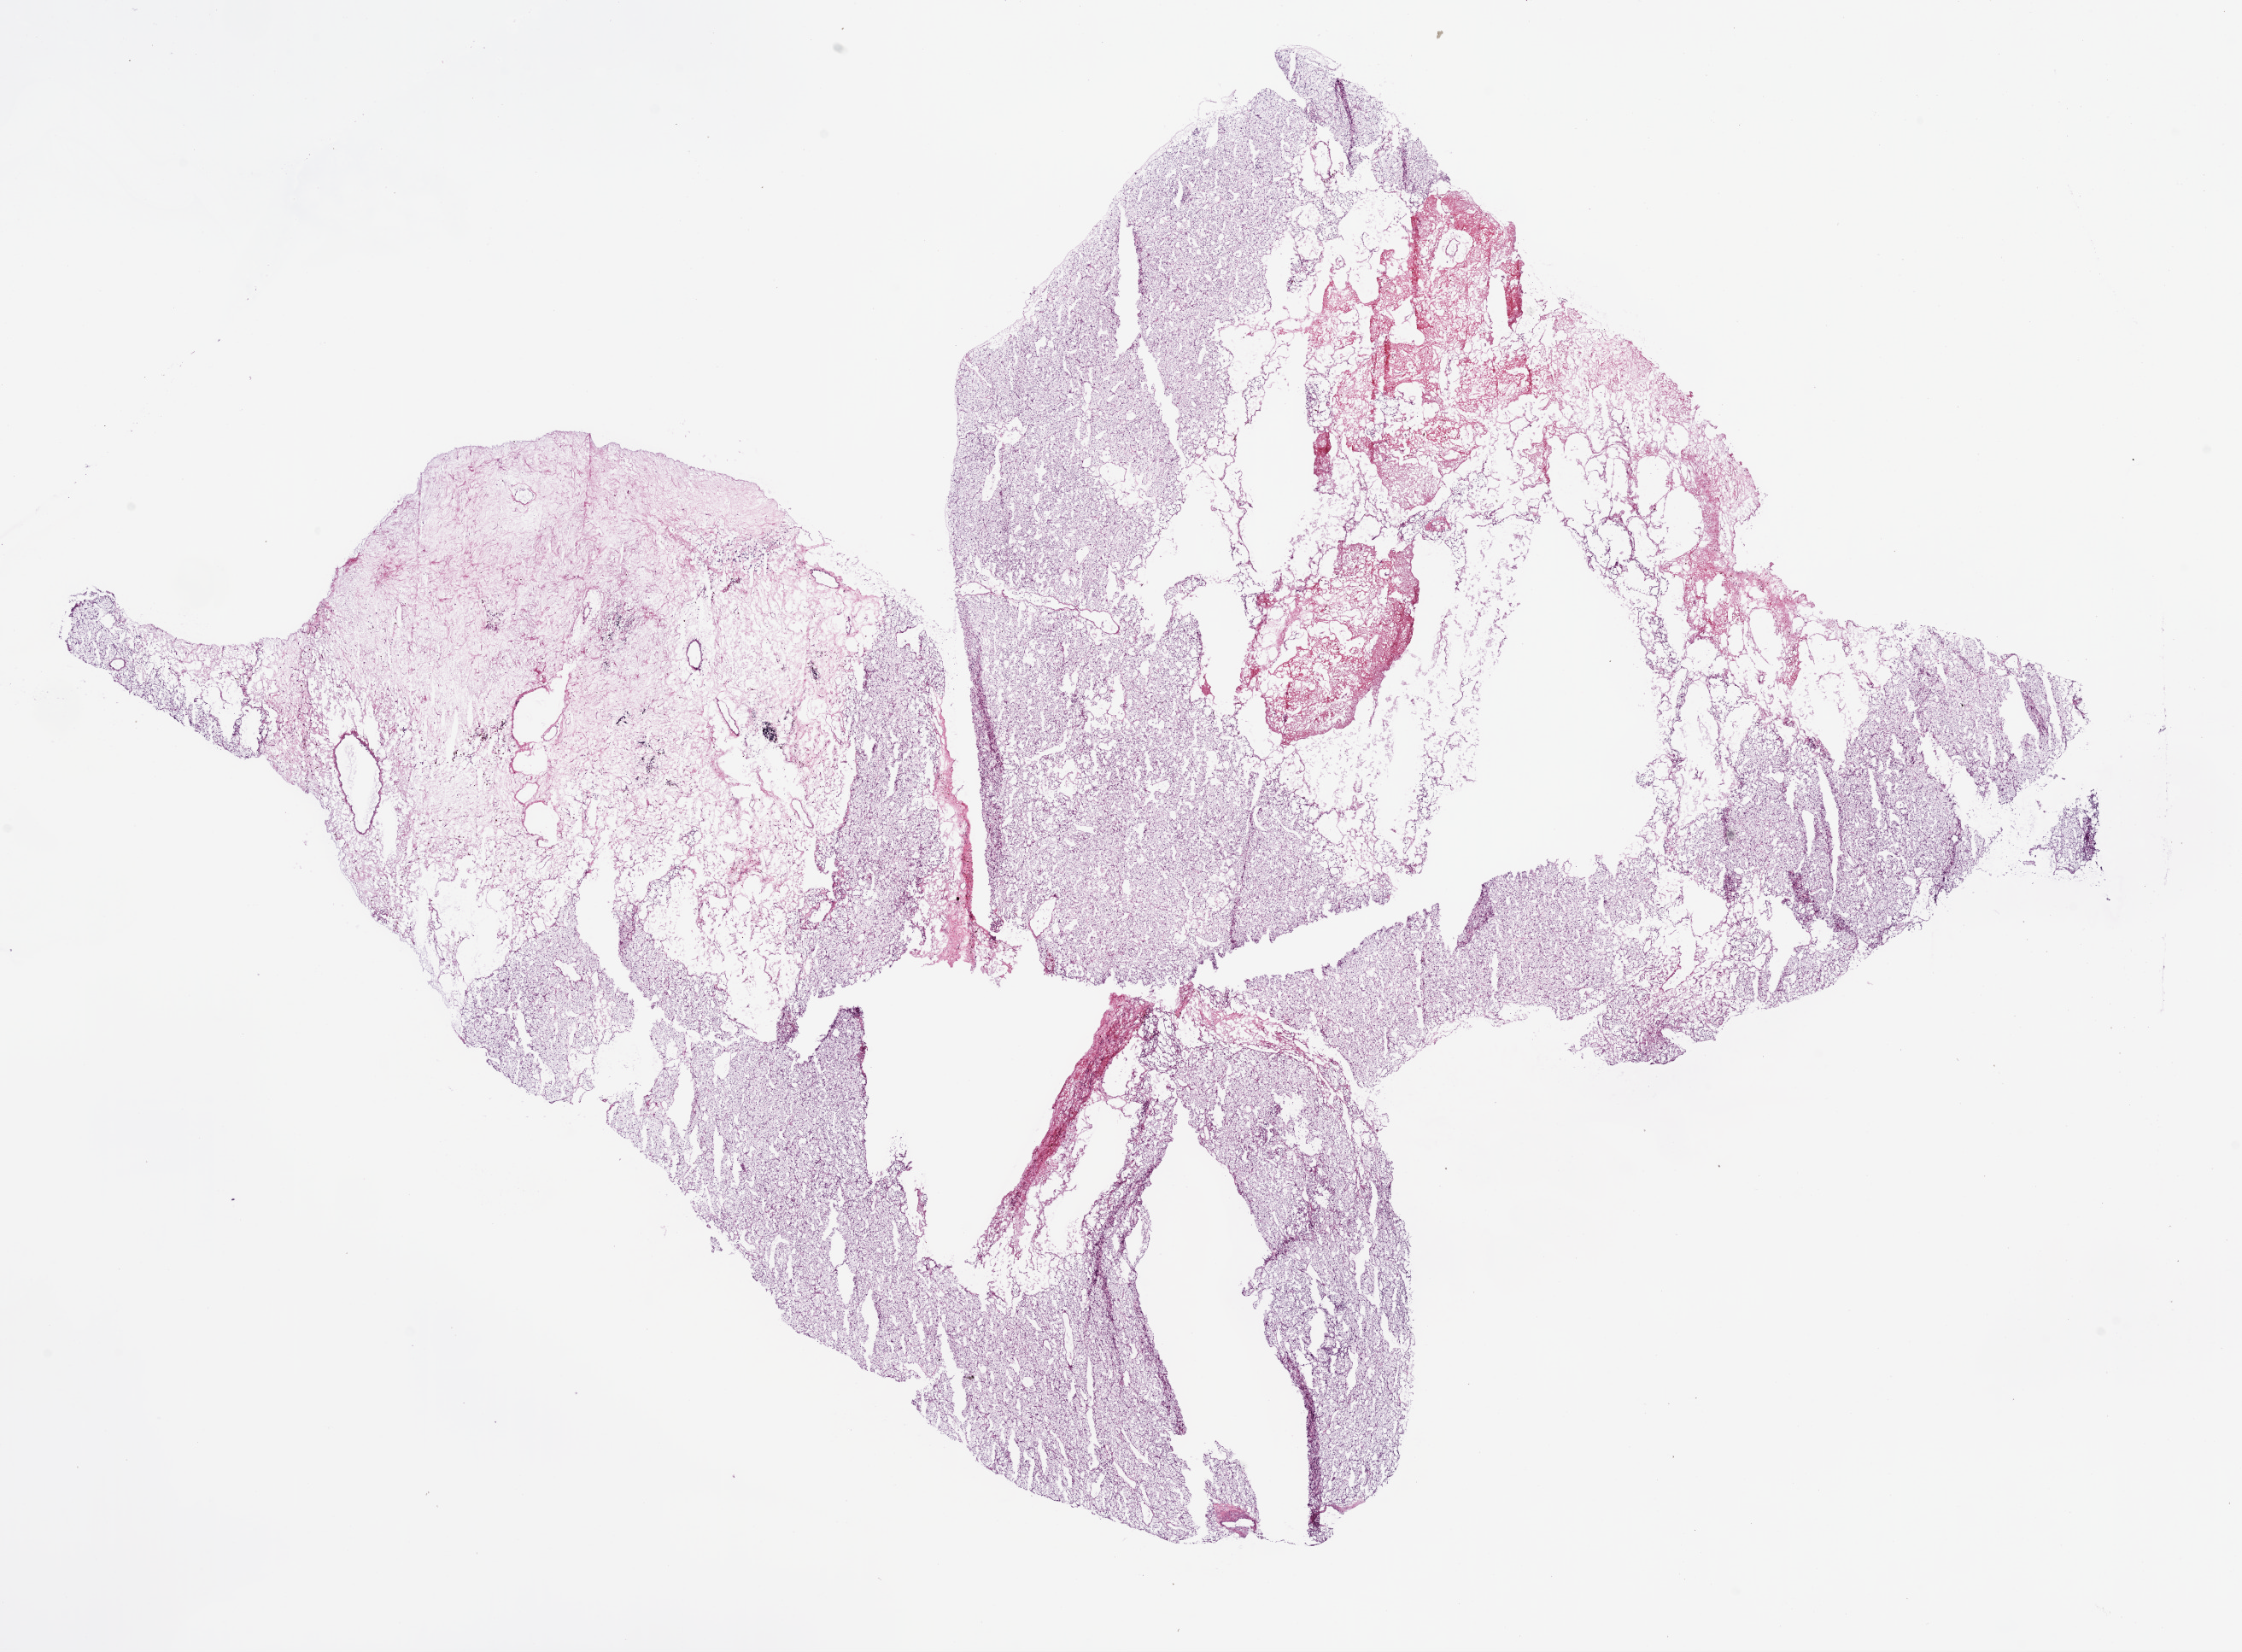
Digitized H&E-stained tissue section (whole slide) — whole scanned area (about 21.1 x 15.5 mm, slide scanned at 20x) shown as a low-resolution overview. Frozen section. Sample: primary tumour, kidney. Male patient; age at initial diagnosis 39 years. Histologic grade: G2 (moderately differentiated). Slide review estimates, as recorded: tumour cells 75%, tumour nuclei 85%, normal cells 0%, stromal cells 25%, necrosis 0%.
Diagnosis: Clear cell adenocarcinoma, NOS. AJCC pathologic stage: I.